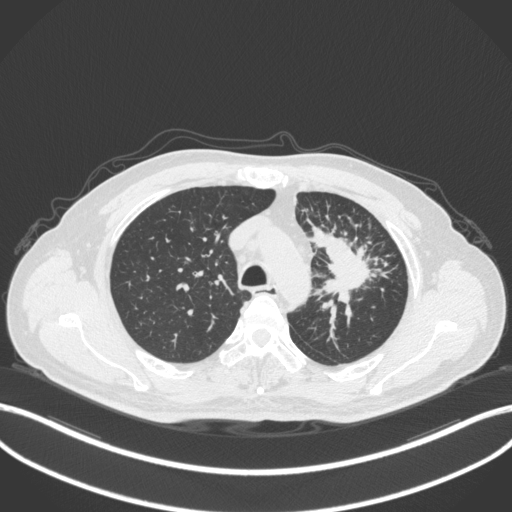
Chest CT, one axial slice; slice 268 of 386 in the series (ordered by position); reconstruction kernel B31f; 120 kVp; lung window (W 1500 / L -600 HU); 1 mm slice thickness; 512 × 512 image matrix, field of view 400 × 400 mm. Patient: male, 69 years. From the clinical record (not read from this slice): clinical TNM (as recorded): T2a N2 M0; histopathological grade: G2-3.
Outlined on this slice (bounding box drawn by a radiologist):
- lung tumour (recorded histology: adenocarcinoma): bounding box (x1, y1, x2, y2) in pixels: (306, 219, 376, 309)